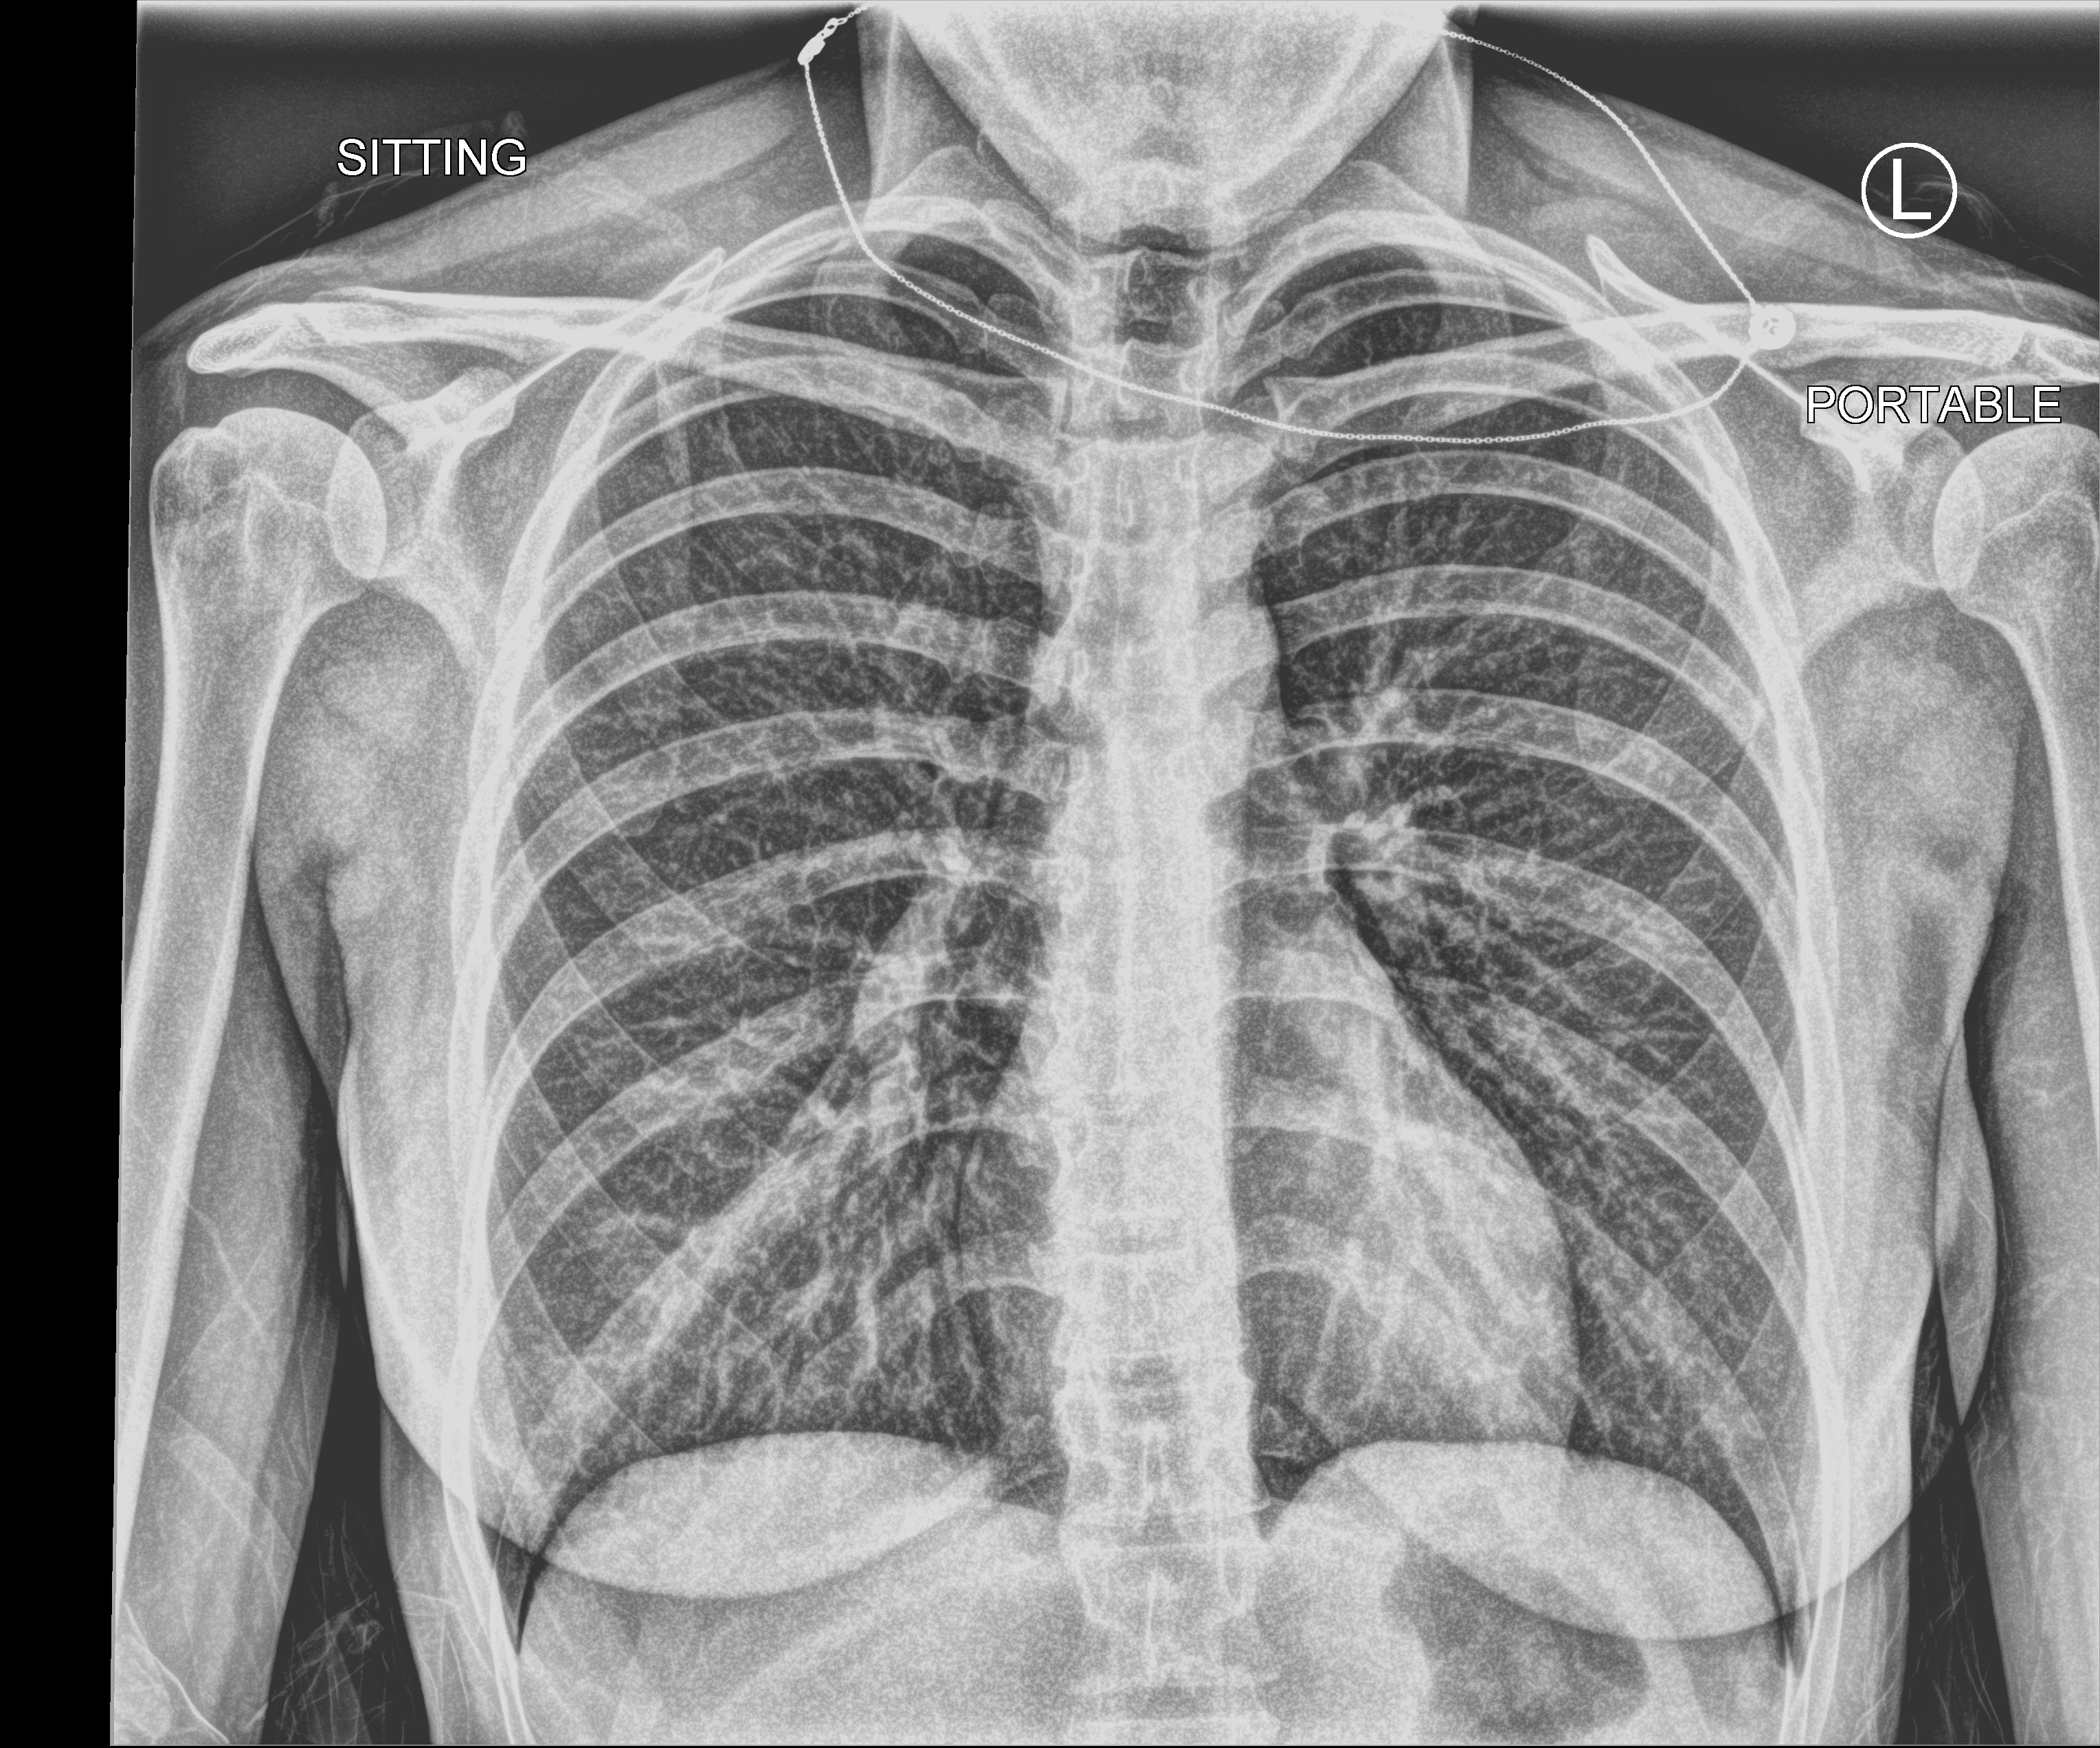
Chest X-ray (portable); anteroposterior (AP) projection. Female patient hospitalised with COVID-19, age 18–59 years.
Admission-level facts for this patient (not findings on this image; timing relative to this image not recorded): diabetes (admission record): no; length of hospital stay: 1 day.